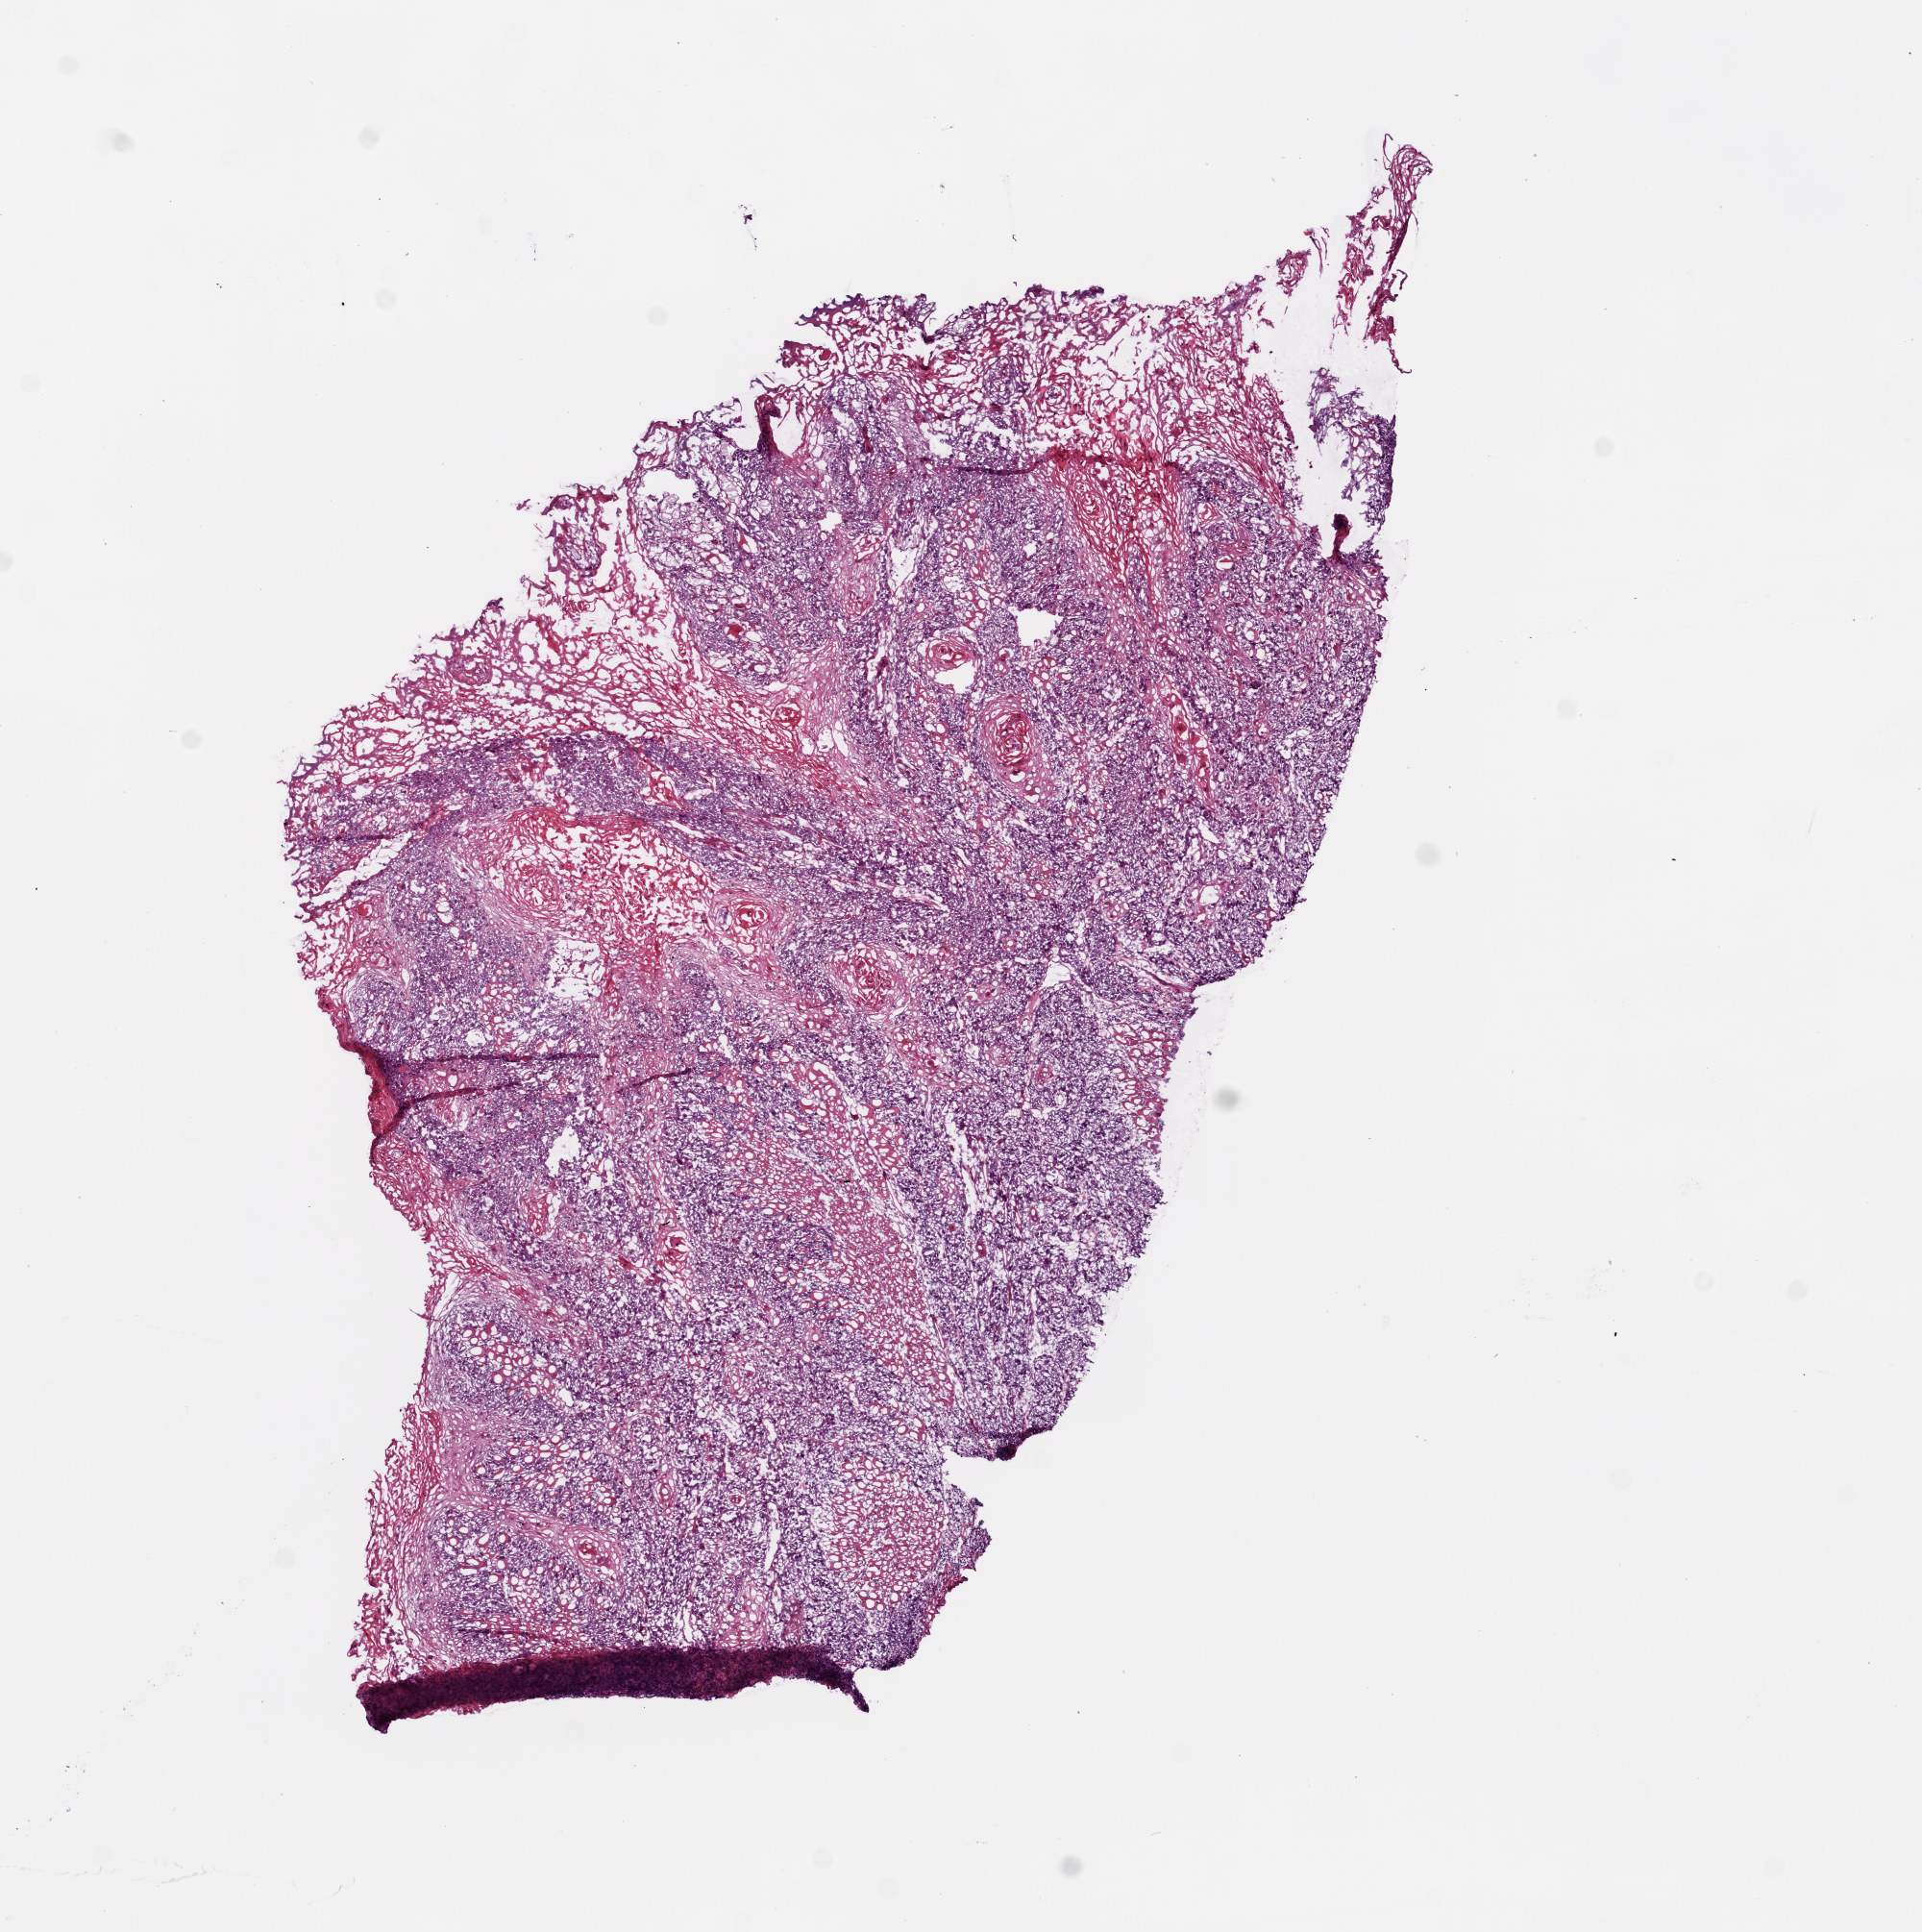
Whole-slide histology image, H&E, whole scanned area (about 8.0 x 8.1 mm, acquisition: 20x scan) shown as a low-resolution overview. Frozen section from the bottom of the tissue portion. Sample: primary tumour, head and neck. Patient: male, age at initial diagnosis 60 years. Histologic grade: G2 (moderately differentiated). Composition of this section per pathologist review: tumour cells 85%, tumour nuclei 85%, normal cells 0%, stromal cells 15%, necrosis 0%.
- AJCC pathologic stage: II
- TNM: T2 N0
- pathologic diagnosis: Squamous cell carcinoma, NOS (tongue, NOS)